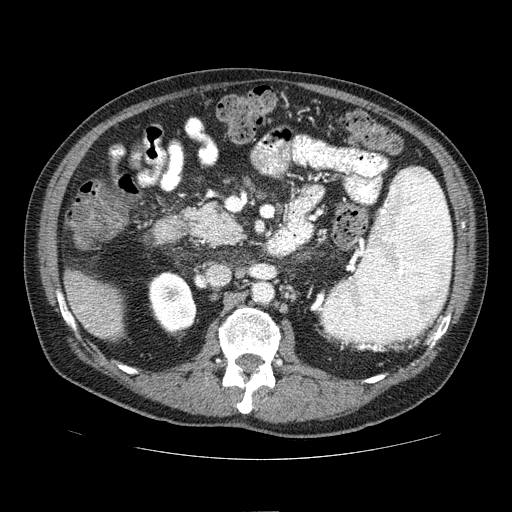
Contrast-enhanced abdominal CT (liver protocol), one axial slice; position 22 of 81 along the scan axis; reconstruction kernel STANDARD; 100 kVp; one of 2 acquisitions stored at this slice position; soft-tissue window (W 400 / L 40 HU); 2.5 mm slice thickness; 512 × 512 image matrix. Case-level facts recorded for this patient, not image findings: diagnosis: hepatocellular carcinoma (patient treated with transarterial chemoembolisation; whether this scan precedes or follows treatment is not stated here); TNM stage (as recorded): Stage-IIIA; Child-Pugh class: A; tumour differentiation: well differentiated; tumour nodularity: multinodular.
Structures marked on this image (semi-automatically segmented with operator editing):
- liver parenchyma outside the tumour (the mass and vessels are separate outlines, so this box may not span the whole liver): bounding box (x1, y1, x2, y2) in pixels: (64, 270, 124, 342)
- liver vessels: (80, 305, 88, 326)